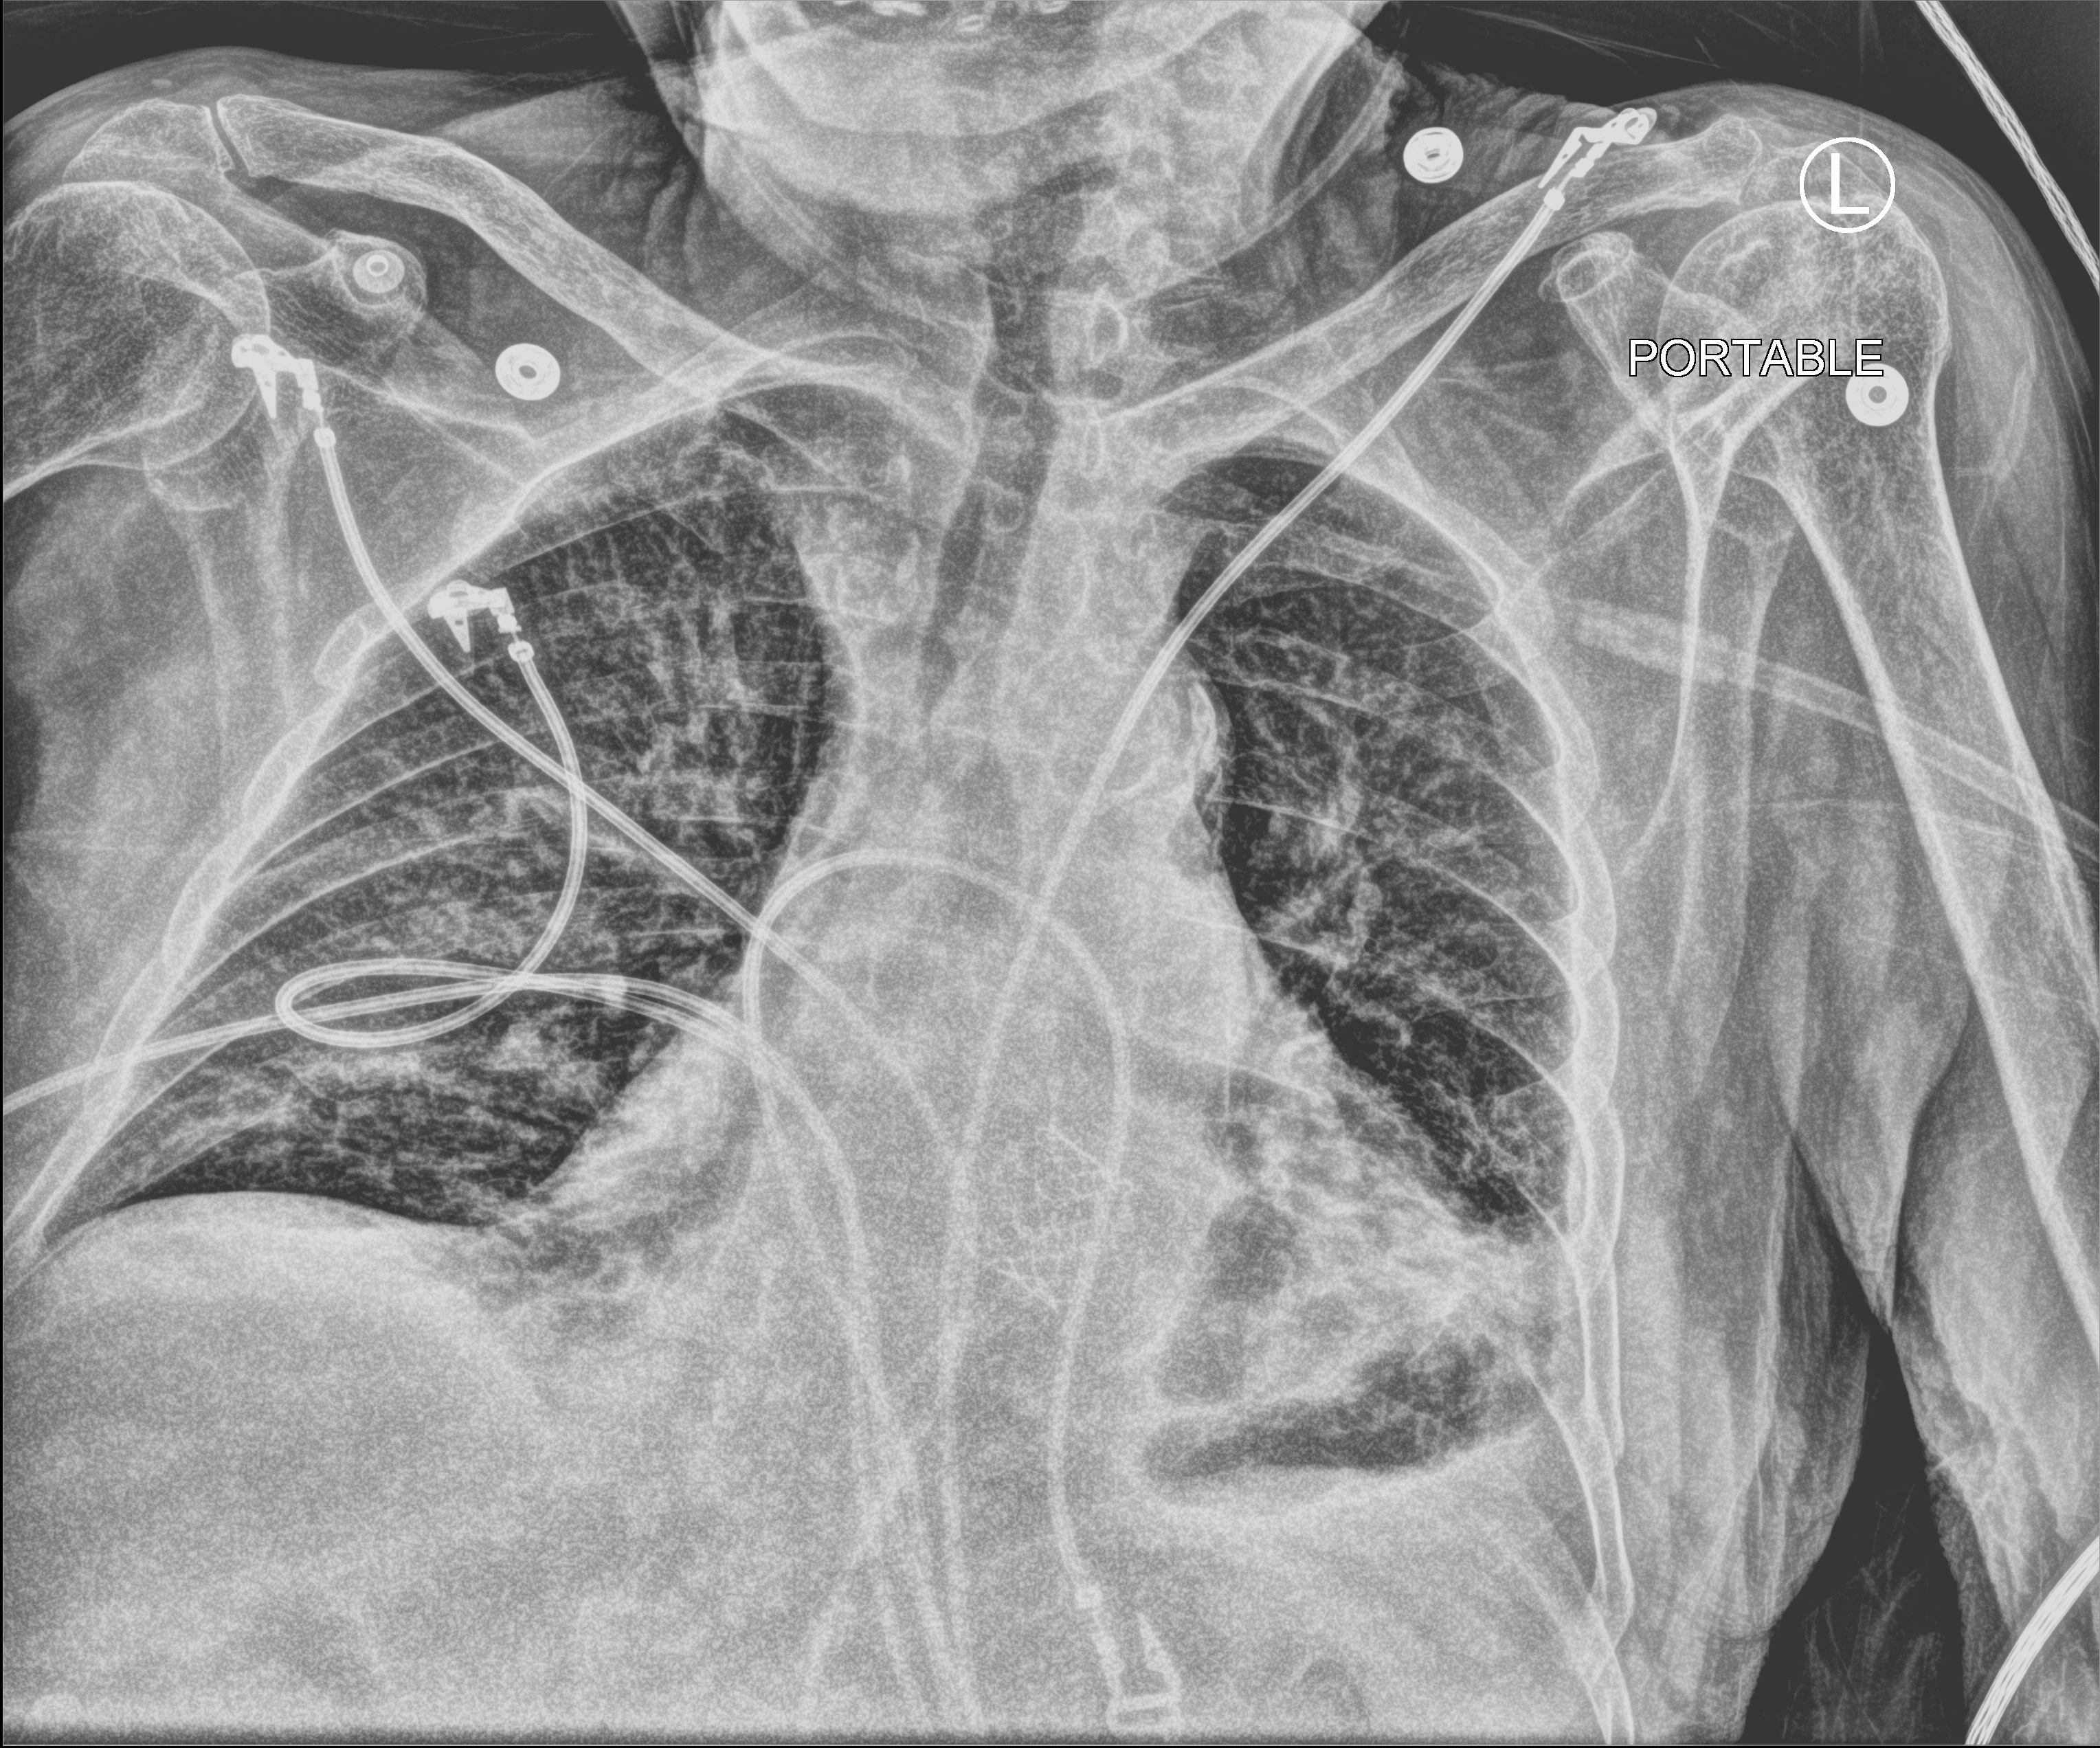
Bedside chest radiograph (computed radiography); anteroposterior (AP) projection. Male patient hospitalised with COVID-19, age 75–90 years.
Hospital-stay facts (about this admission, not read from this image; timing relative to this image not recorded):
- mechanically ventilated during this hospital stay: no